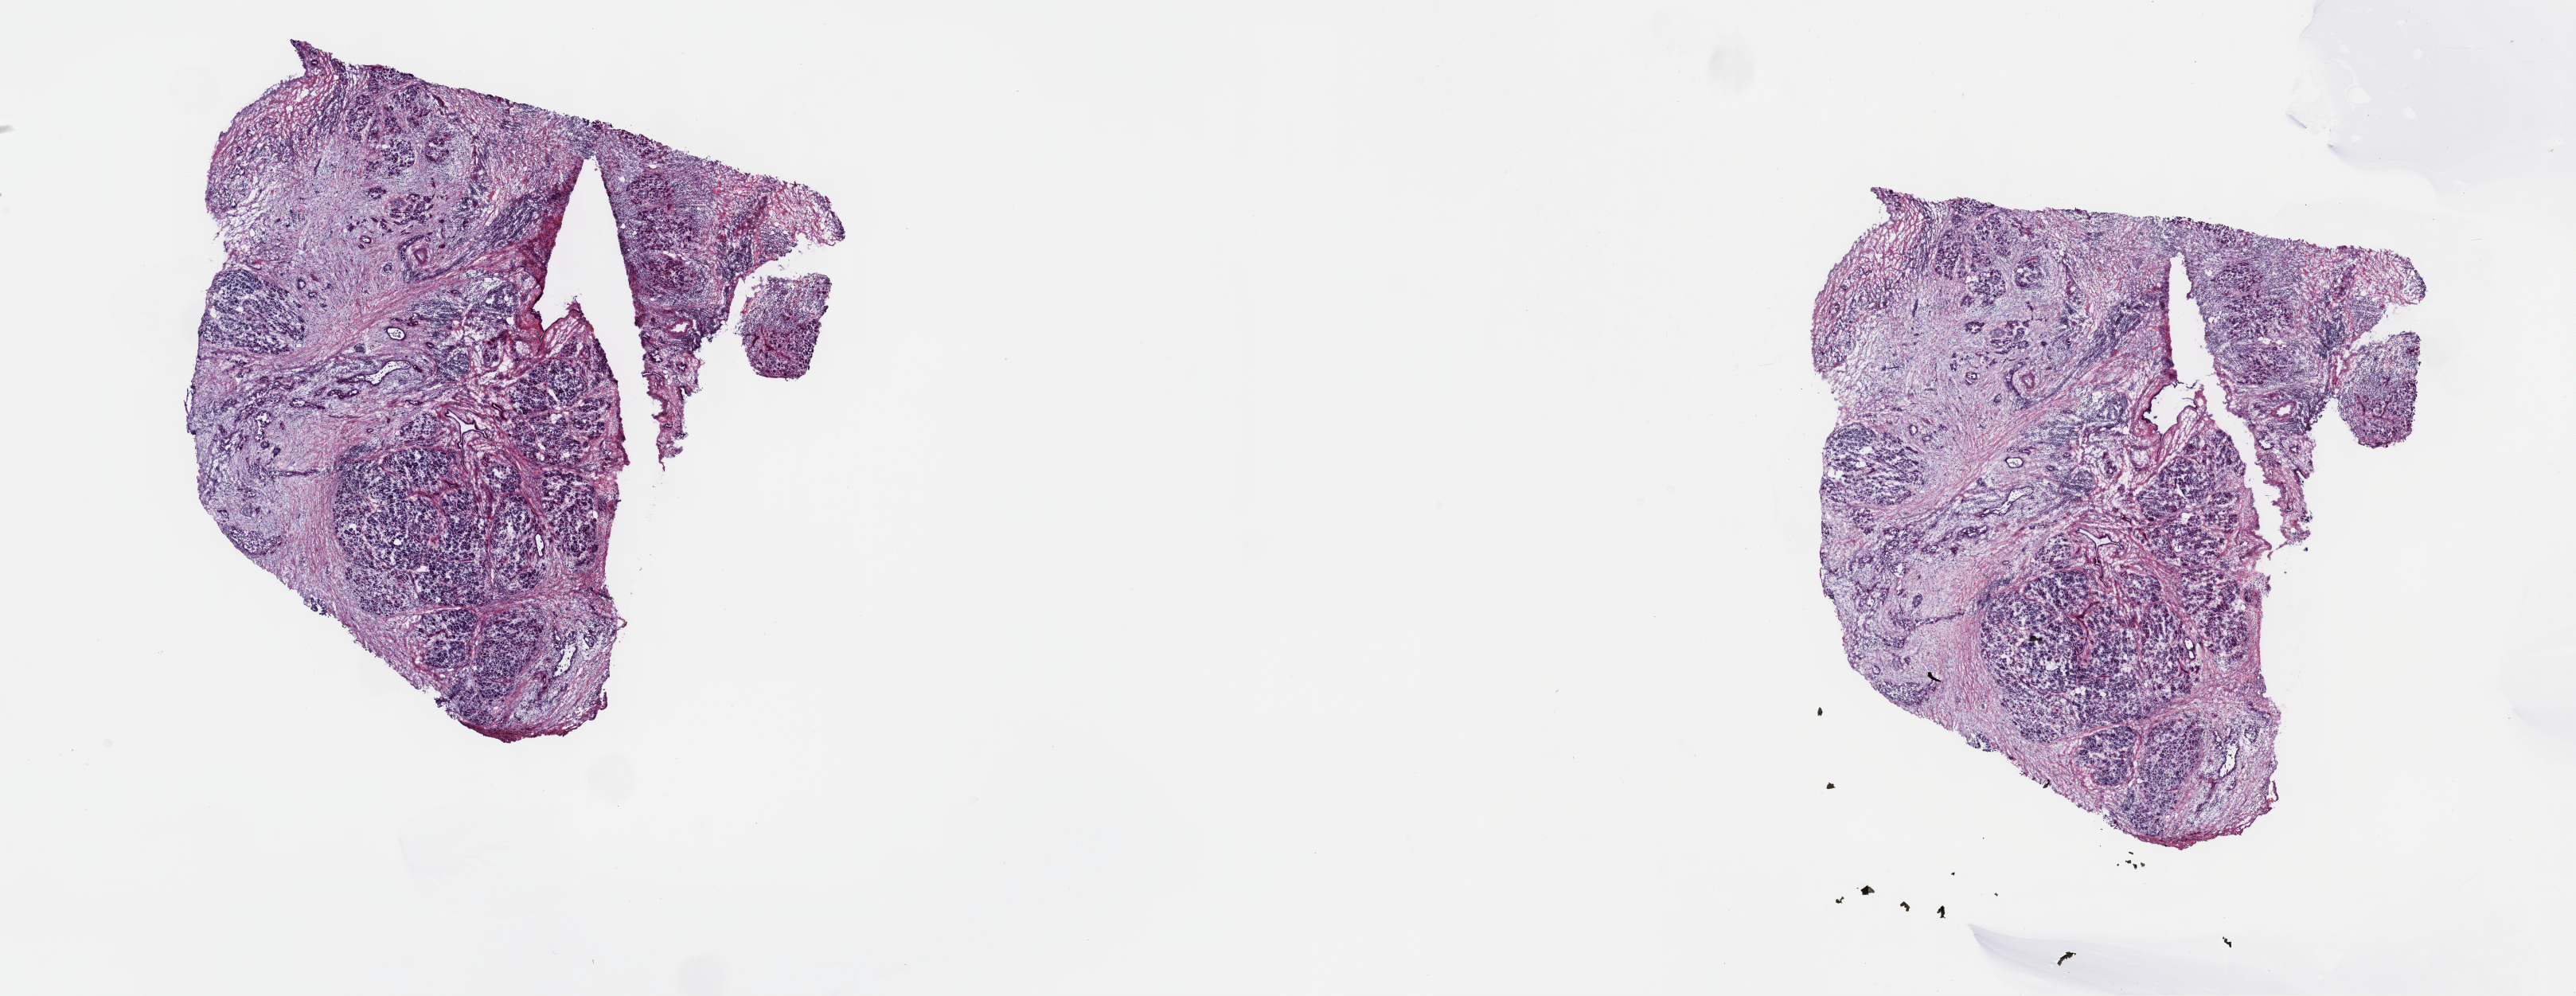
H&E whole-slide image — a low-resolution overview of the entire scanned area, about 26.2 x 10.1 mm (acquisition: 40x scan). Frozen section from the top of the tissue portion. Pancreas, primary tumour sample. Patient: female, age at initial diagnosis 60 years. Histologic grade: G3 (poorly differentiated). Composition of this section per pathologist review: tumour cells 35%, tumour nuclei 20%, normal cells 65%, stromal cells 0%, necrosis 0%. Inflammatory infiltration, as recorded: lymphocyte infiltration 8%, monocyte infiltration 0%, neutrophil infiltration 0%.
Diagnosis: Infiltrating duct carcinoma, NOS (overlapping lesion of pancreas). AJCC pathologic stage: IIA (7th edition). Lymph nodes positive (case pathology): 0 of 14 examined.